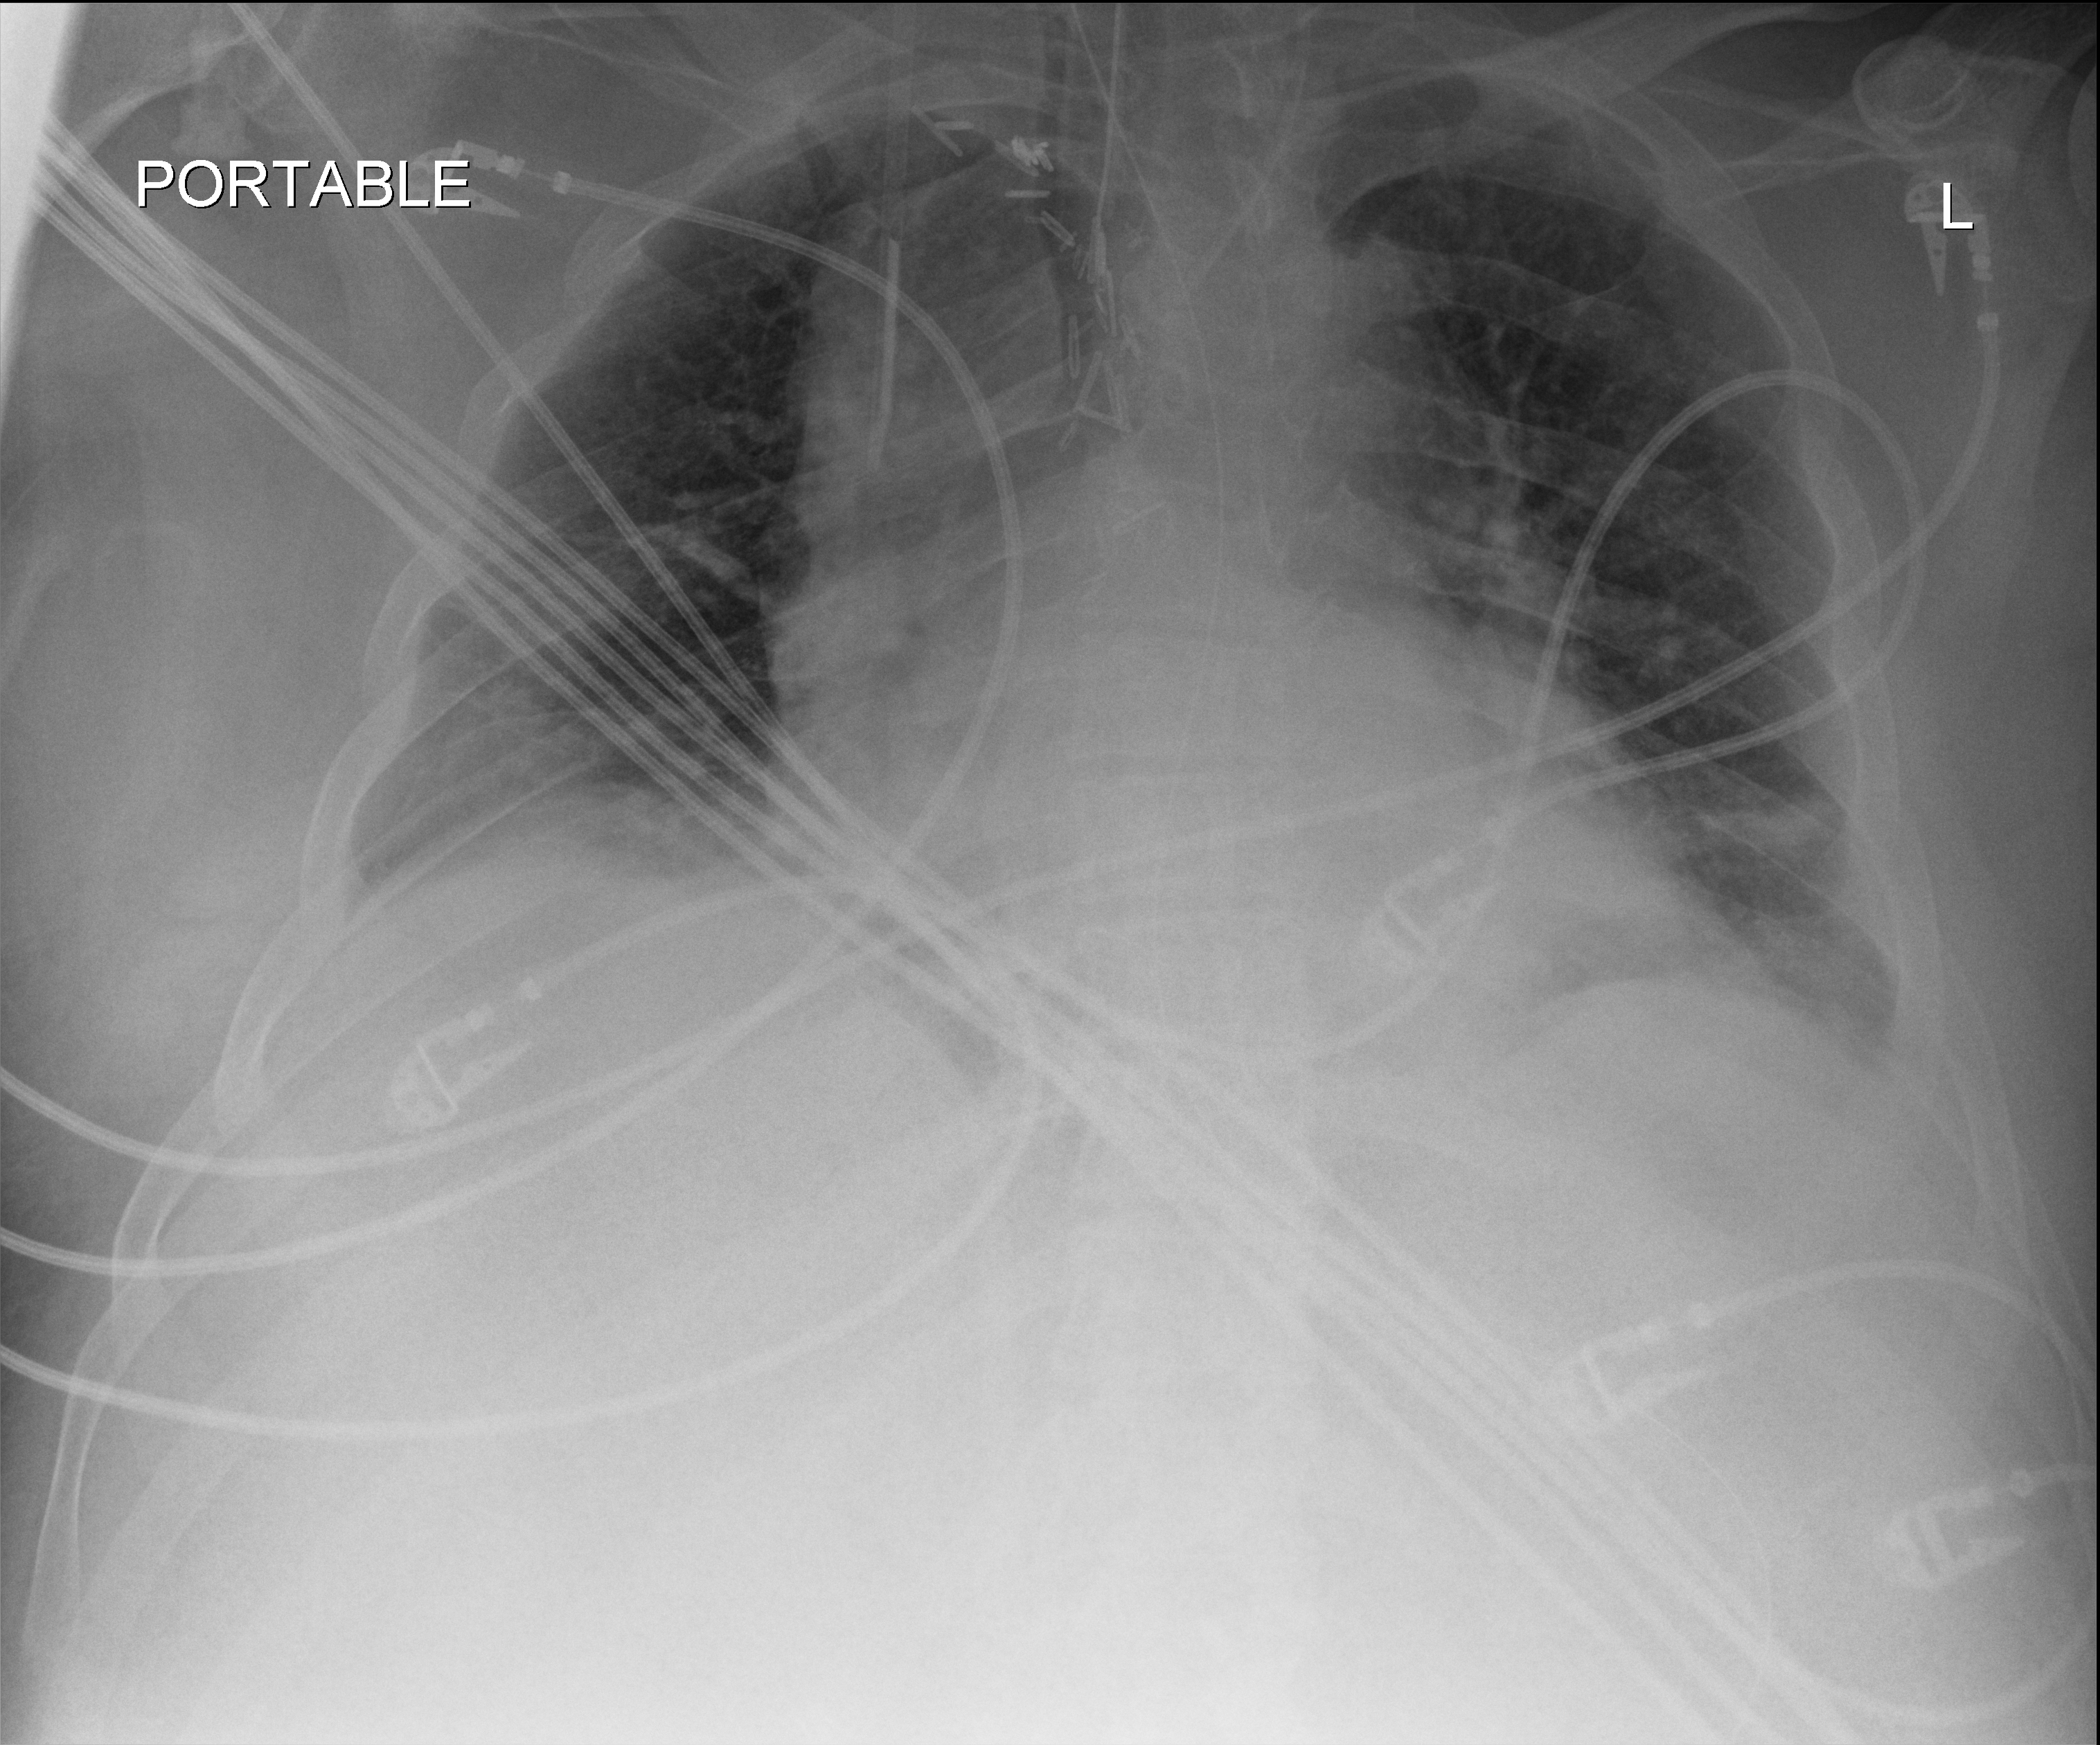
Chest X-ray (portable); anteroposterior (AP) projection. Adult patient hospitalised with COVID-19, age 18–59 years.
Admission-level facts for this patient (not findings on this image; timing relative to this image not recorded):
- length of hospital stay: 2 days
- admitted to intensive care during this hospital stay: yes
- mechanically ventilated during this hospital stay: yes